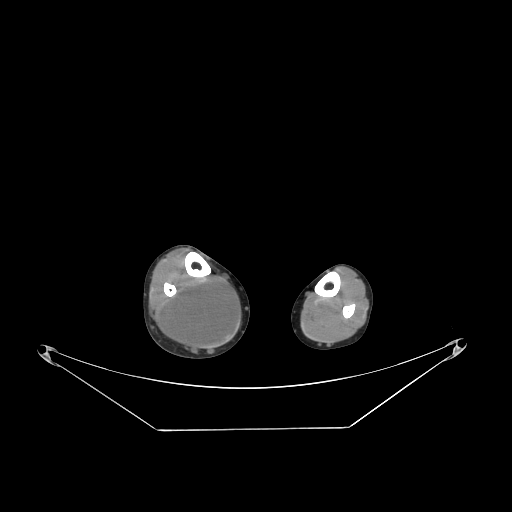
CT of an extremity soft-tissue mass (from a PET/CT study), one axial slice. Slice 81 of 267 in the series (ordered by position). Soft-tissue window (W 400 / L 40 HU). 3.75 mm slice thickness. 512 × 512 image matrix, field of view 500 × 500 mm. Male patient. From the clinical record (not read from this slice): histological type: liposarcoma - round cell; grade: high; site of the primary tumour: right calf.
Annotated regions visible in this slice (expert contour drawn on MRI and transferred to this co-registered scan by the dataset authors):
- gross tumour volume (mass): box from (x=164, y=278) to (x=239, y=346) px